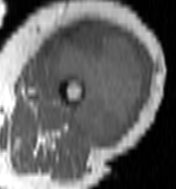
MRI of an extremity soft-tissue mass, one axial slice. Slice 54 of 100 in the series (ordered by position). MR volume resampled by the dataset authors to the PET/CT grid (not the native acquisition matrix). 176 × 189 image matrix, field of view 172 × 185 mm. Female patient. Case-level facts recorded for this patient, not image findings: histological type: undifferentiated – high grade; grade: high; site of the primary tumour: left thigh.
Outlined on this slice (expert contour drawn on MRI and transferred to this co-registered scan by the dataset authors):
- gross tumour volume including surrounding oedema: bounding box (x1, y1, x2, y2) in pixels: (48, 25, 145, 143)
- gross tumour volume (mass): (48, 25, 145, 143)